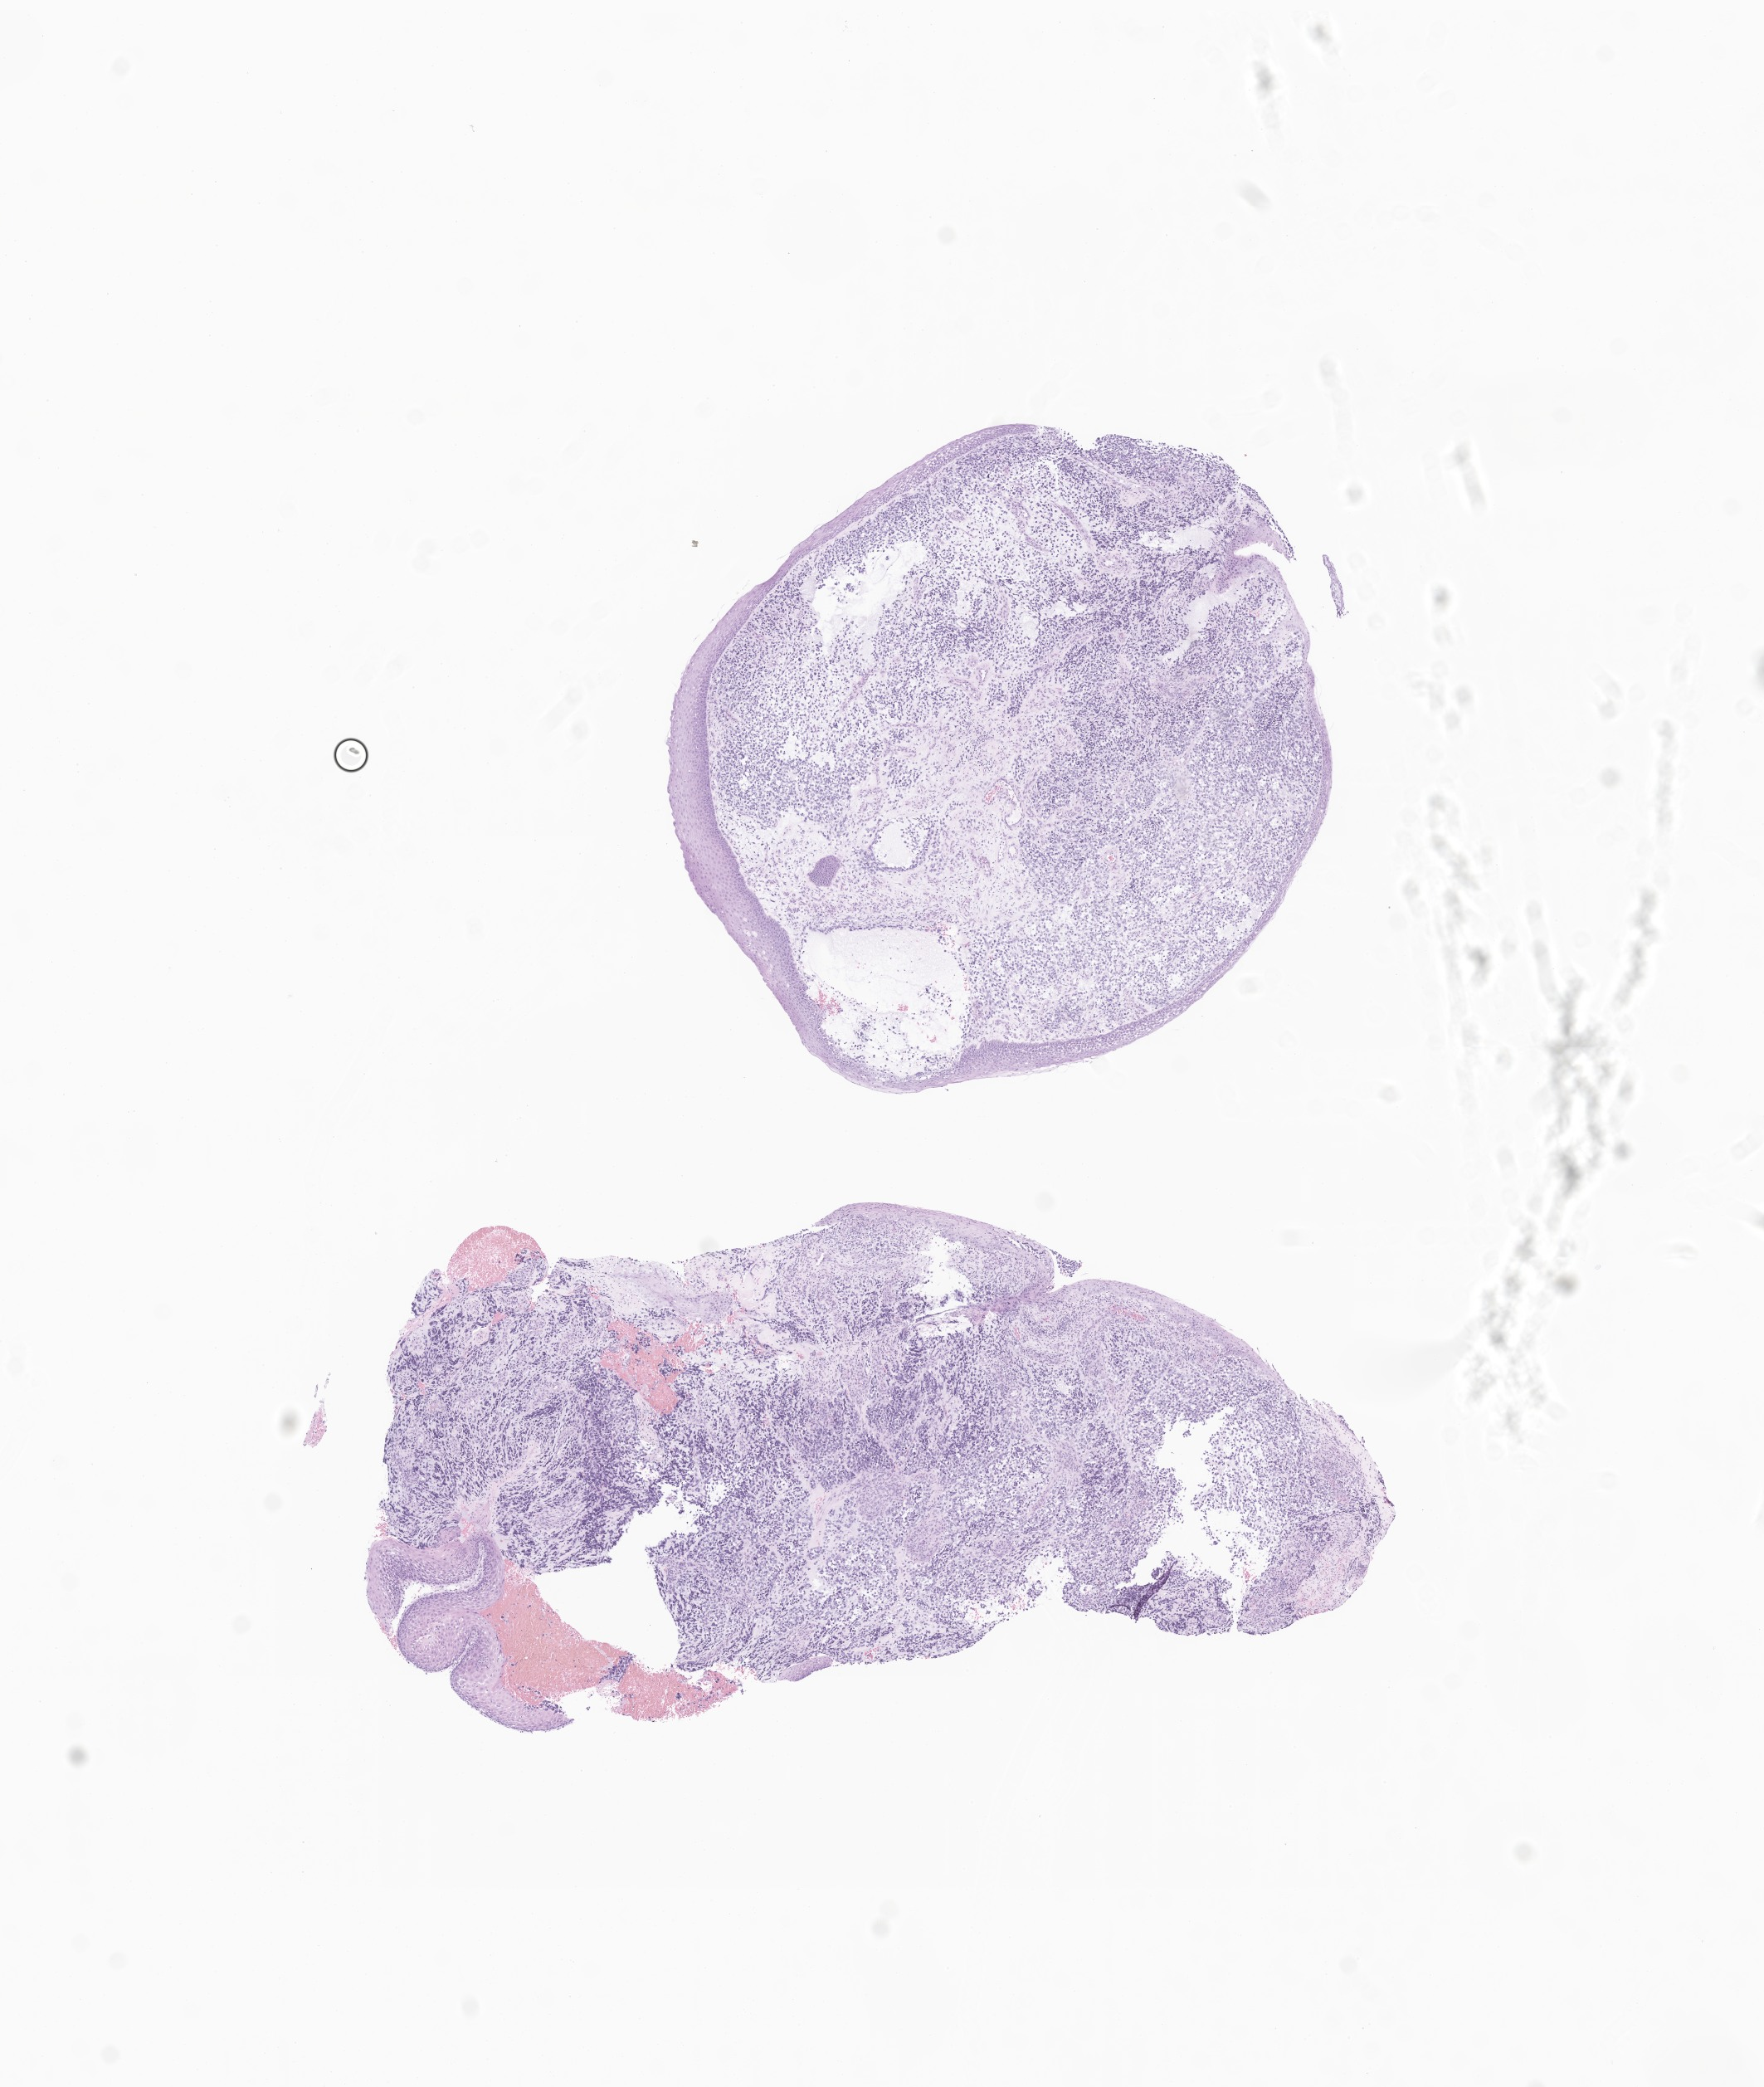
Whole-slide image, hematoxylin and eosin (H&E) stain of tumor tissue from the larynx, whole scanned area (about 9.0 x 10.6 mm) shown as a low-resolution overview; formalin-fixed paraffin-embedded section. Patient: male, age 64 months (5 years 4 months).
Diagnosis (ICD-O-3 morphology term): Rhabdomyosarcoma, NOS.